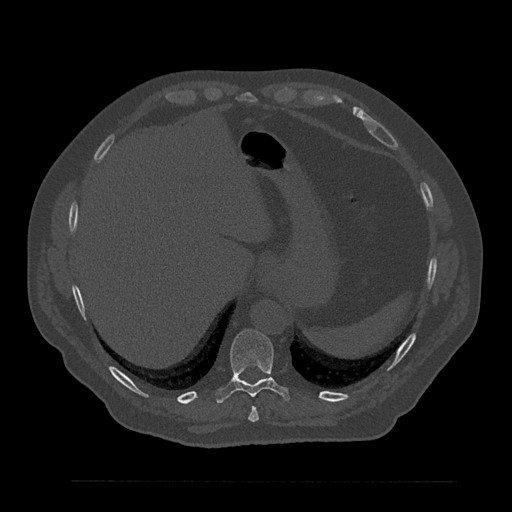
CT including the spine, one axial slice; reconstruction kernel Br40s/3; 120 kVp; bone window (W 1800 / L 400 HU); 0.5 mm slice thickness; 512 × 512 image matrix. Patient: male, 61 years. Case-level facts recorded for this patient, not image findings: primary cancer: prostate.
Annotated regions visible in this slice (semi-automatic segmentation, software-assisted and operator-edited):
- T10 vertebra: bounding box <216,329,290,403> (left, top, right, bottom; pixels)
- T9 vertebra: <248,406,259,422>